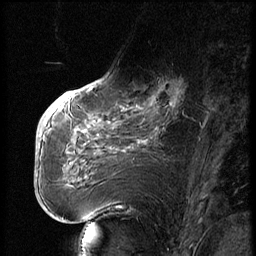
Breast MRI (dynamic contrast-enhanced), one sagittal slice. Slice 26 of 74 in the series (ordered by position). Dynamic contrast-enhanced series, image 2 of 3 at this slice position (ordered by acquisition). 1.5 T. TE 4.2 ms, TR 9 ms. 2.5 mm slice thickness. 256 × 256 image matrix, field of view 180 × 180 mm. Patient: female, 56 years. From the clinical record (not read from this slice): setting: breast cancer imaged before/during neoadjuvant chemotherapy.
Outlined on this slice (semi-automatic segmentation, software-assisted and operator-edited):
- analysis volume of interest (the breast-tissue region the enhancement analysis was run in; not a lesion): box from (x=123, y=71) to (x=195, y=131) px
- tumour enhancement mask (voxels above the 140 % enhancement threshold inside the analysis volume of interest): (x=149, y=80)–(x=183, y=122)